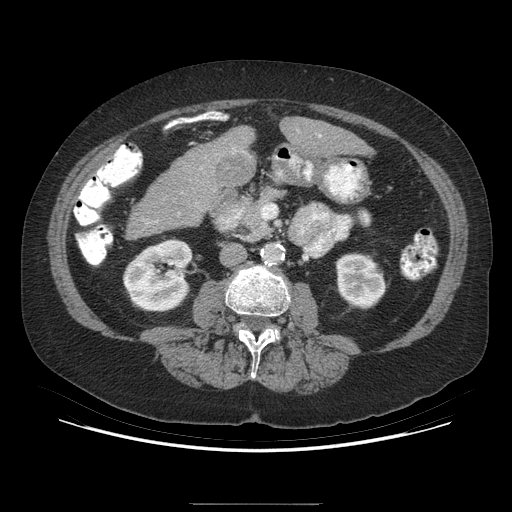
Contrast-enhanced abdominal CT (liver protocol), one axial slice. Slice 130 of 192 in the series (ordered by position). 140 kVp. Soft-tissue window (W 400 / L 40 HU). 2.5 mm slice thickness. 512 × 512 image matrix, field of view 400 × 400 mm. From the clinical record (not read from this slice): diagnosis: hepatocellular carcinoma (patient treated with transarterial chemoembolisation; whether this scan precedes or follows treatment is not stated here); TNM stage (as recorded): Stage-I; Child-Pugh class: A; tumour nodularity: uninodular; tumour size: 3.2 cm.
Annotated regions visible in this slice (semi-automatic segmentation, software-assisted and operator-edited):
- liver parenchyma outside the tumour (the mass and vessels are separate outlines, so this box may not span the whole liver): bounding box [x1, y1, x2, y2] px = [280, 118, 358, 156]
- mass: [213, 150, 256, 186]
- liver vessels: [319, 135, 321, 137]